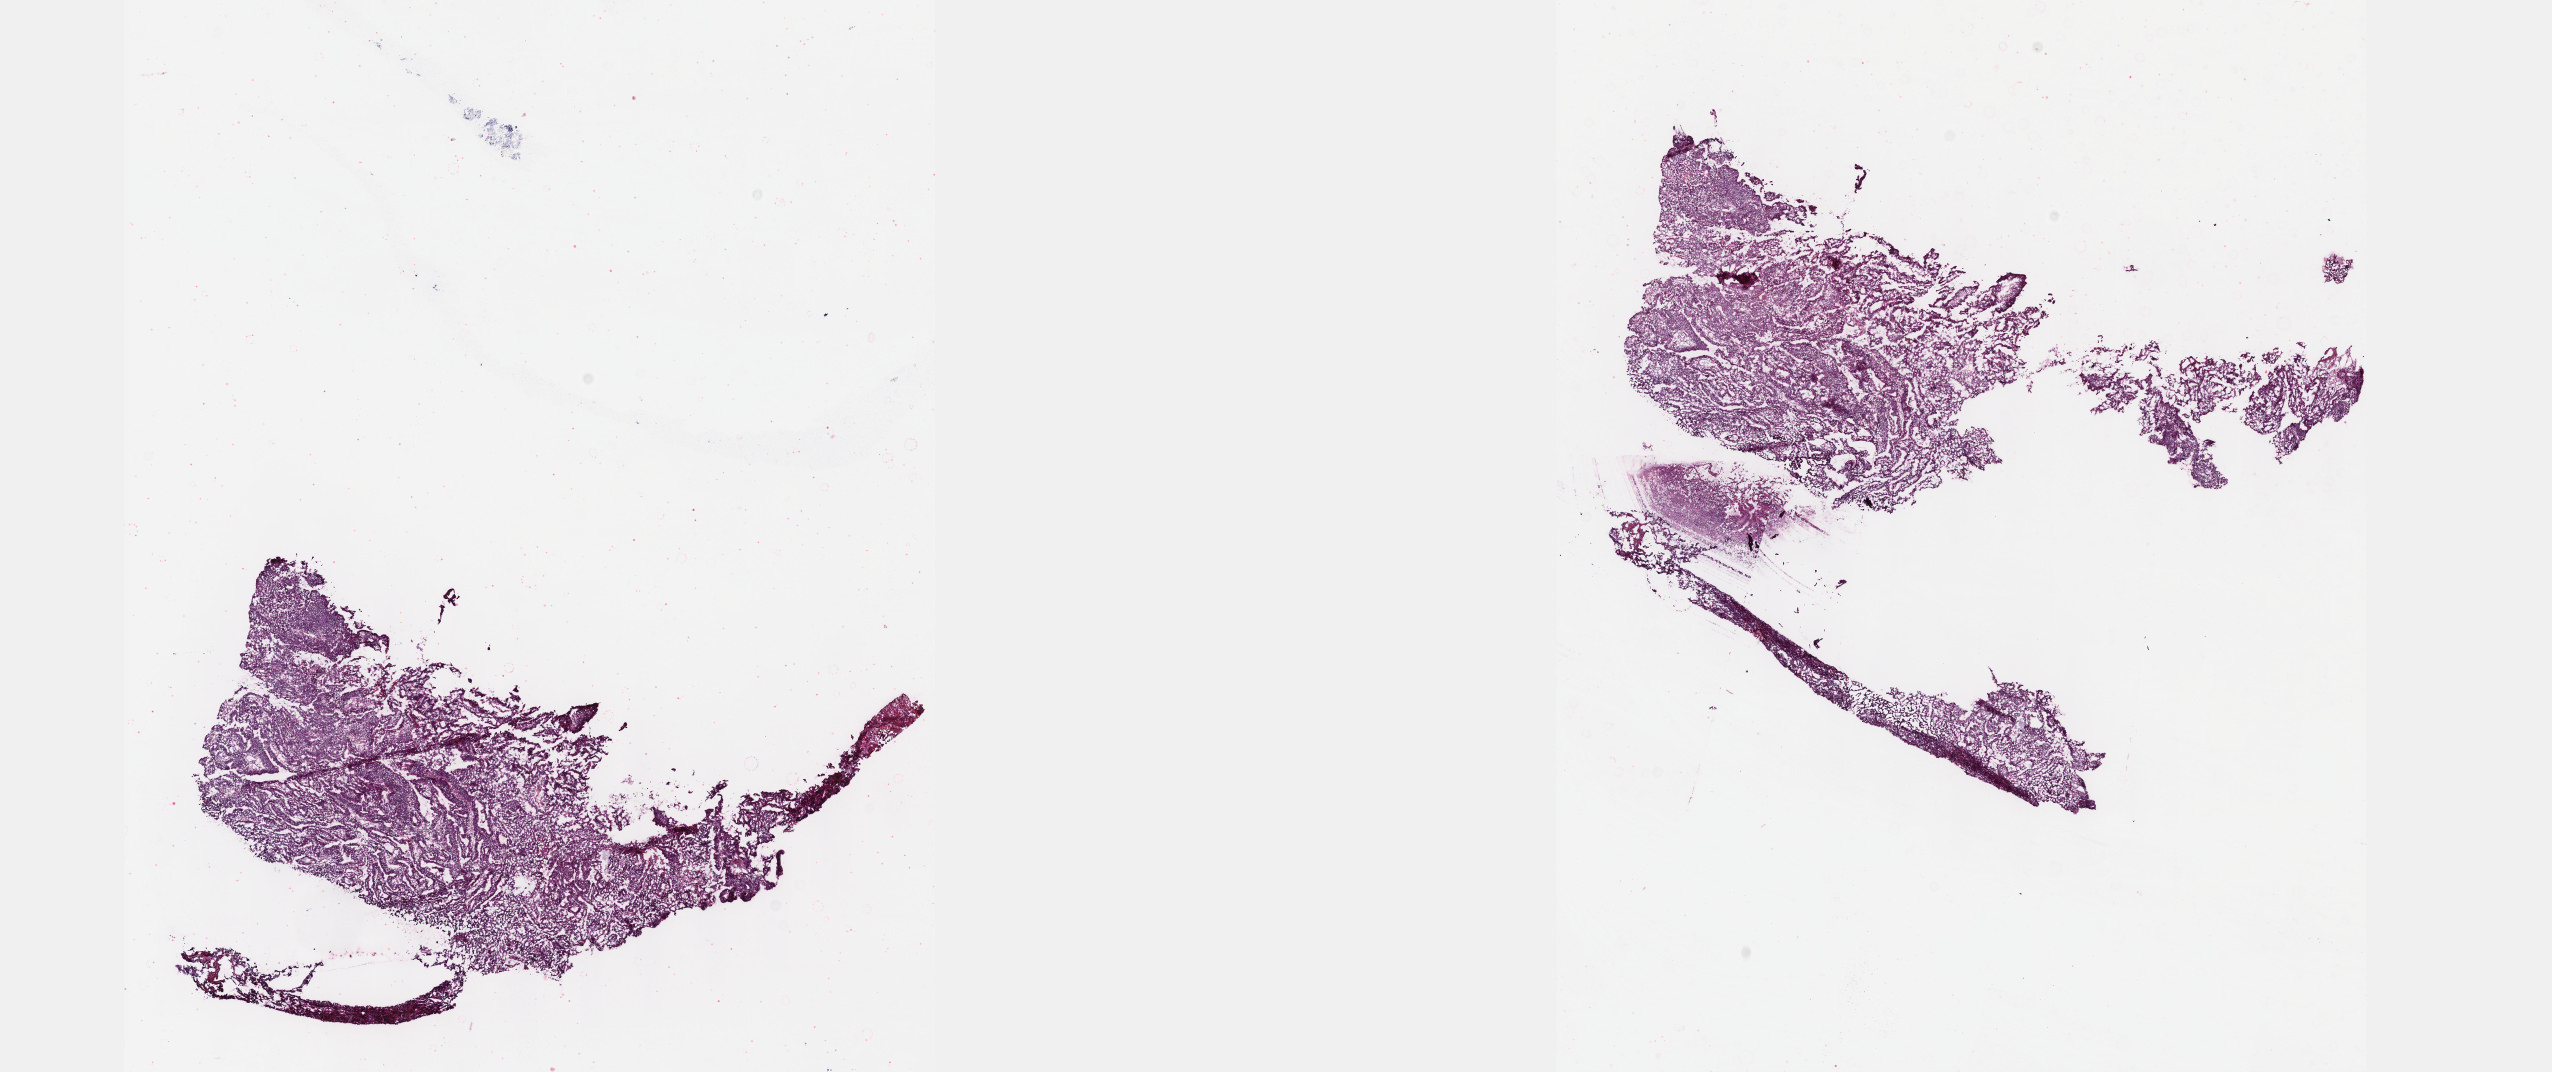
Whole-slide histology image, Hematoxylin and eosin (H&E) stained — whole scanned area (about 20.6 x 8.7 mm, from a 40x scan) shown as a low-resolution overview. Frozen section. Primary tumour sample from the rectum. Patient: male, age at initial diagnosis 66 years.
Pathologic diagnosis: Adenocarcinoma, NOS.